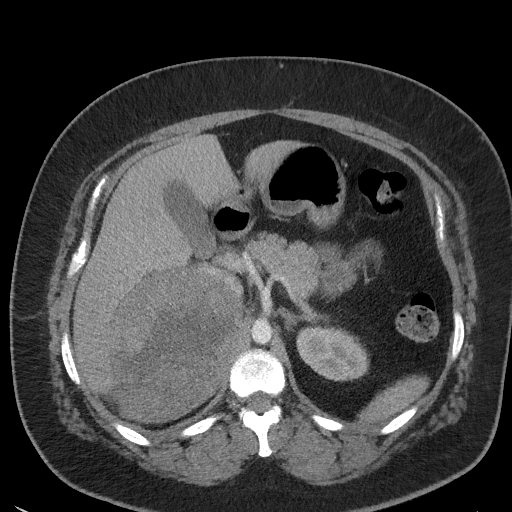
Contrast-enhanced abdominal CT, one axial slice; position 32 of 56 along the scan axis; reconstruction kernel I41f/3; 120 kVp; intravenous contrast given; soft-tissue window (W 400 / L 40 HU); 512 × 512 image matrix, field of view 373 × 373 mm. Patient: female, 35 years. Case-level facts recorded for this patient, not image findings: diagnosis: adrenocortical carcinoma; tumour side: right adrenal; tumour size at pathology: 15 cm; Ki-67 index: 40 %; stage (as recorded): 2.
Annotated regions visible in this slice (semi-automatically segmented with operator editing):
- mass: bounding box [x1, y1, x2, y2] px = [111, 270, 237, 421]